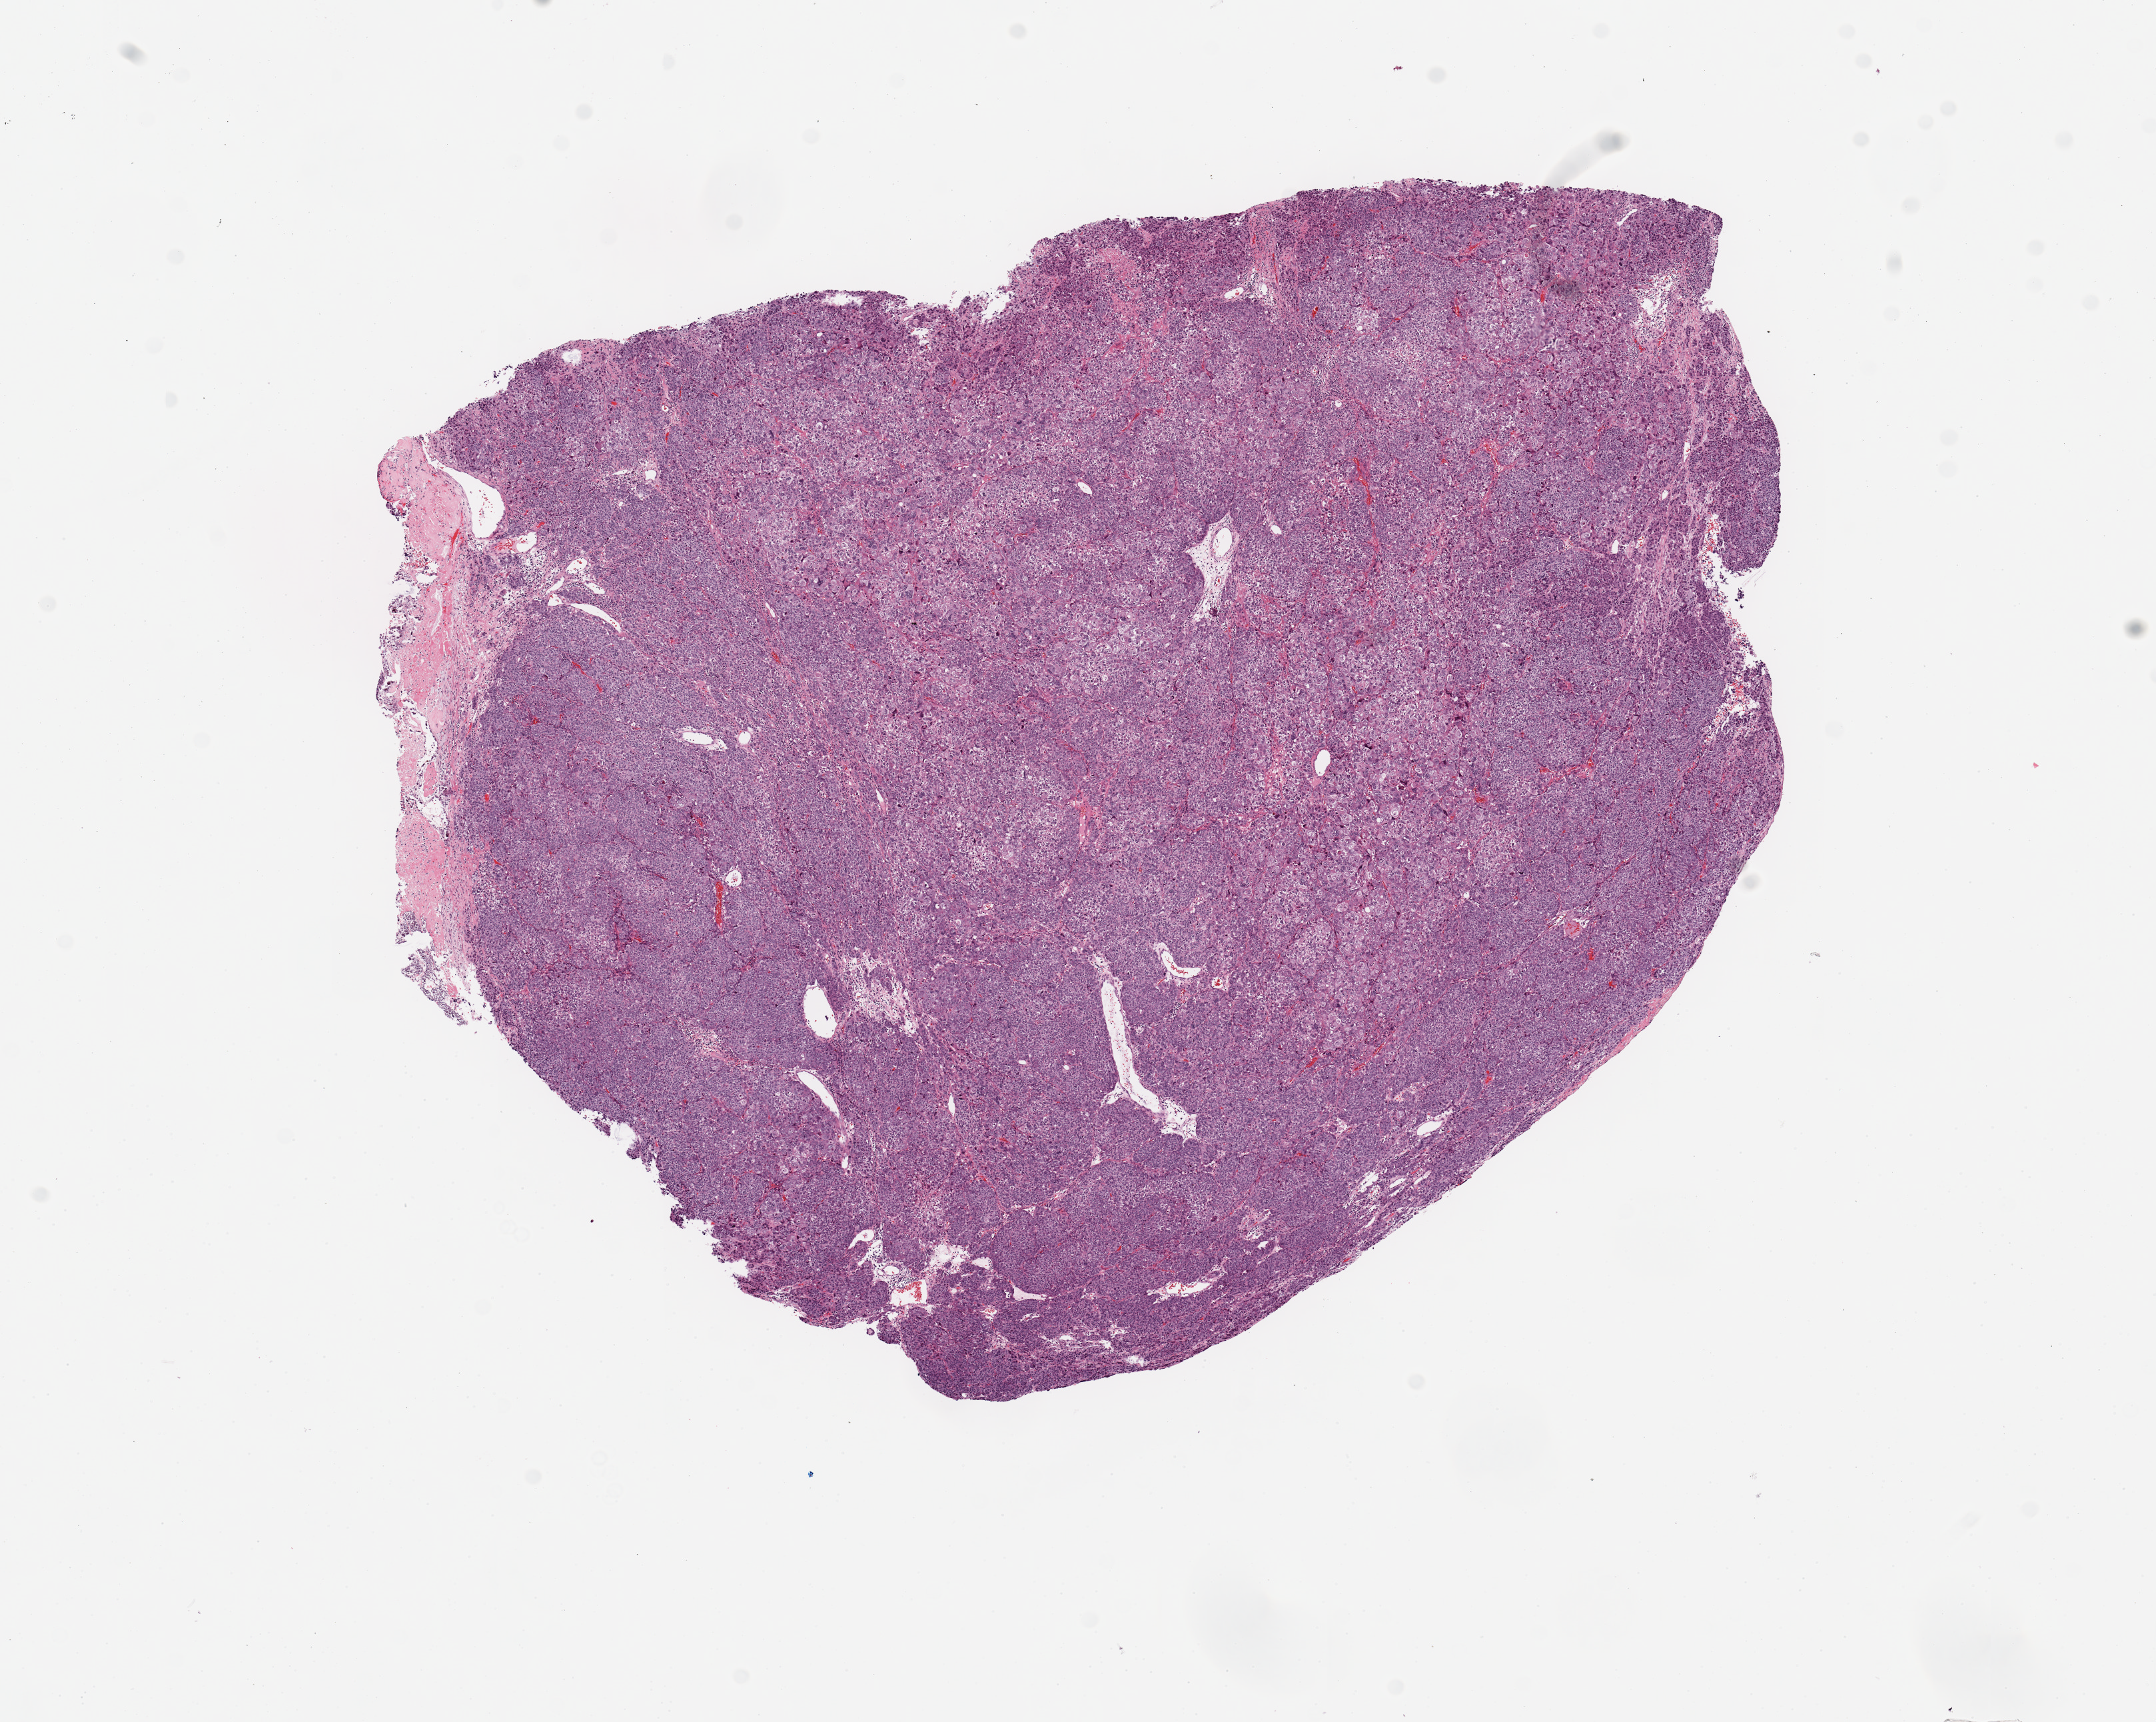
Digitized H&E-stained tissue section (whole slide) — whole scanned area (about 12.8 x 10.2 mm, from a 20x scan) shown as a low-resolution overview, uterus, tumour tissue. Female, 63 y/o. Histologic grade: G3 (poorly differentiated).
AJCC pathologic stage: I. Histologic diagnosis: Endometrioid adenocarcinoma, NOS.